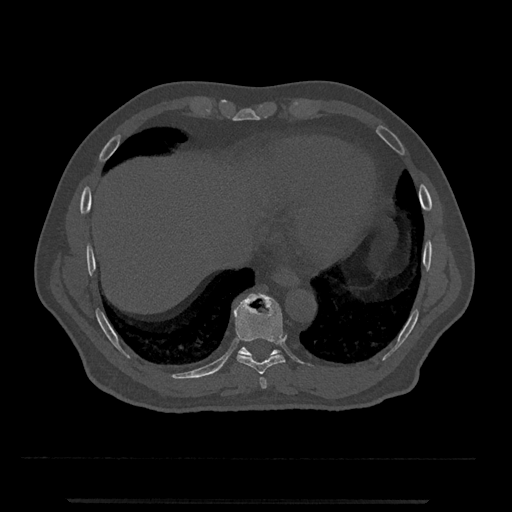
CT including the spine, one axial slice; position 559 of 797 along the scan axis; reconstruction kernel Br40s/3; bone window (W 1800 / L 400 HU); 0.5 mm slice thickness; 512 × 512 image matrix, field of view 419 × 419 mm. Male patient, age 63 years. Case-level facts recorded for this patient, not image findings: primary cancer: prostate.
Annotated regions visible in this slice (semi-automatically segmented with operator editing):
- T10 vertebra: box from (x=238, y=347) to (x=281, y=358) px
- T8 vertebra: (x=259, y=377)–(x=267, y=389)
- T9 vertebra: (x=234, y=293)–(x=285, y=374)